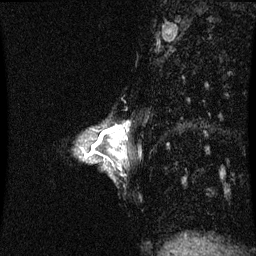
Breast MRI (dynamic contrast-enhanced), one sagittal slice; position 22 of 60 along the scan axis; dynamic contrast-enhanced series, image 2 of 3 at this slice position (ordered by acquisition); 1.5 T; TE 4.2 ms, TR 8.9 ms; 256 × 256 image matrix, field of view 200 × 200 mm. Female patient, age 33 years. Case-level facts recorded for this patient, not image findings: setting: breast cancer imaged before/during neoadjuvant chemotherapy; receptor status: HER2-positive.
Structures marked on this image (semi-automatic segmentation, software-assisted and operator-edited):
- analysis volume of interest (the breast-tissue region the enhancement analysis was run in; not a lesion): bounding box (x1, y1, x2, y2) in pixels: (95, 128, 125, 153)
- tumour enhancement mask (voxels above the 70 % enhancement threshold inside the analysis volume of interest): (95, 130, 111, 147)